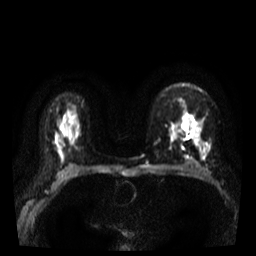
Breast MRI, one axial slice; slice 26 of 39 in the series (ordered by position); diffusion-weighted series; image 2 of 4 stored at this slice position (different b-values; order by instance number); 3 T; 5 mm slice thickness; 256 × 256 image matrix, field of view 320 × 320 mm. Female patient.
Annotated regions visible in this slice (manually delineated by an expert):
- tumour on diffusion-weighted imaging: bounding box <195,122,199,125> (left, top, right, bottom; pixels)